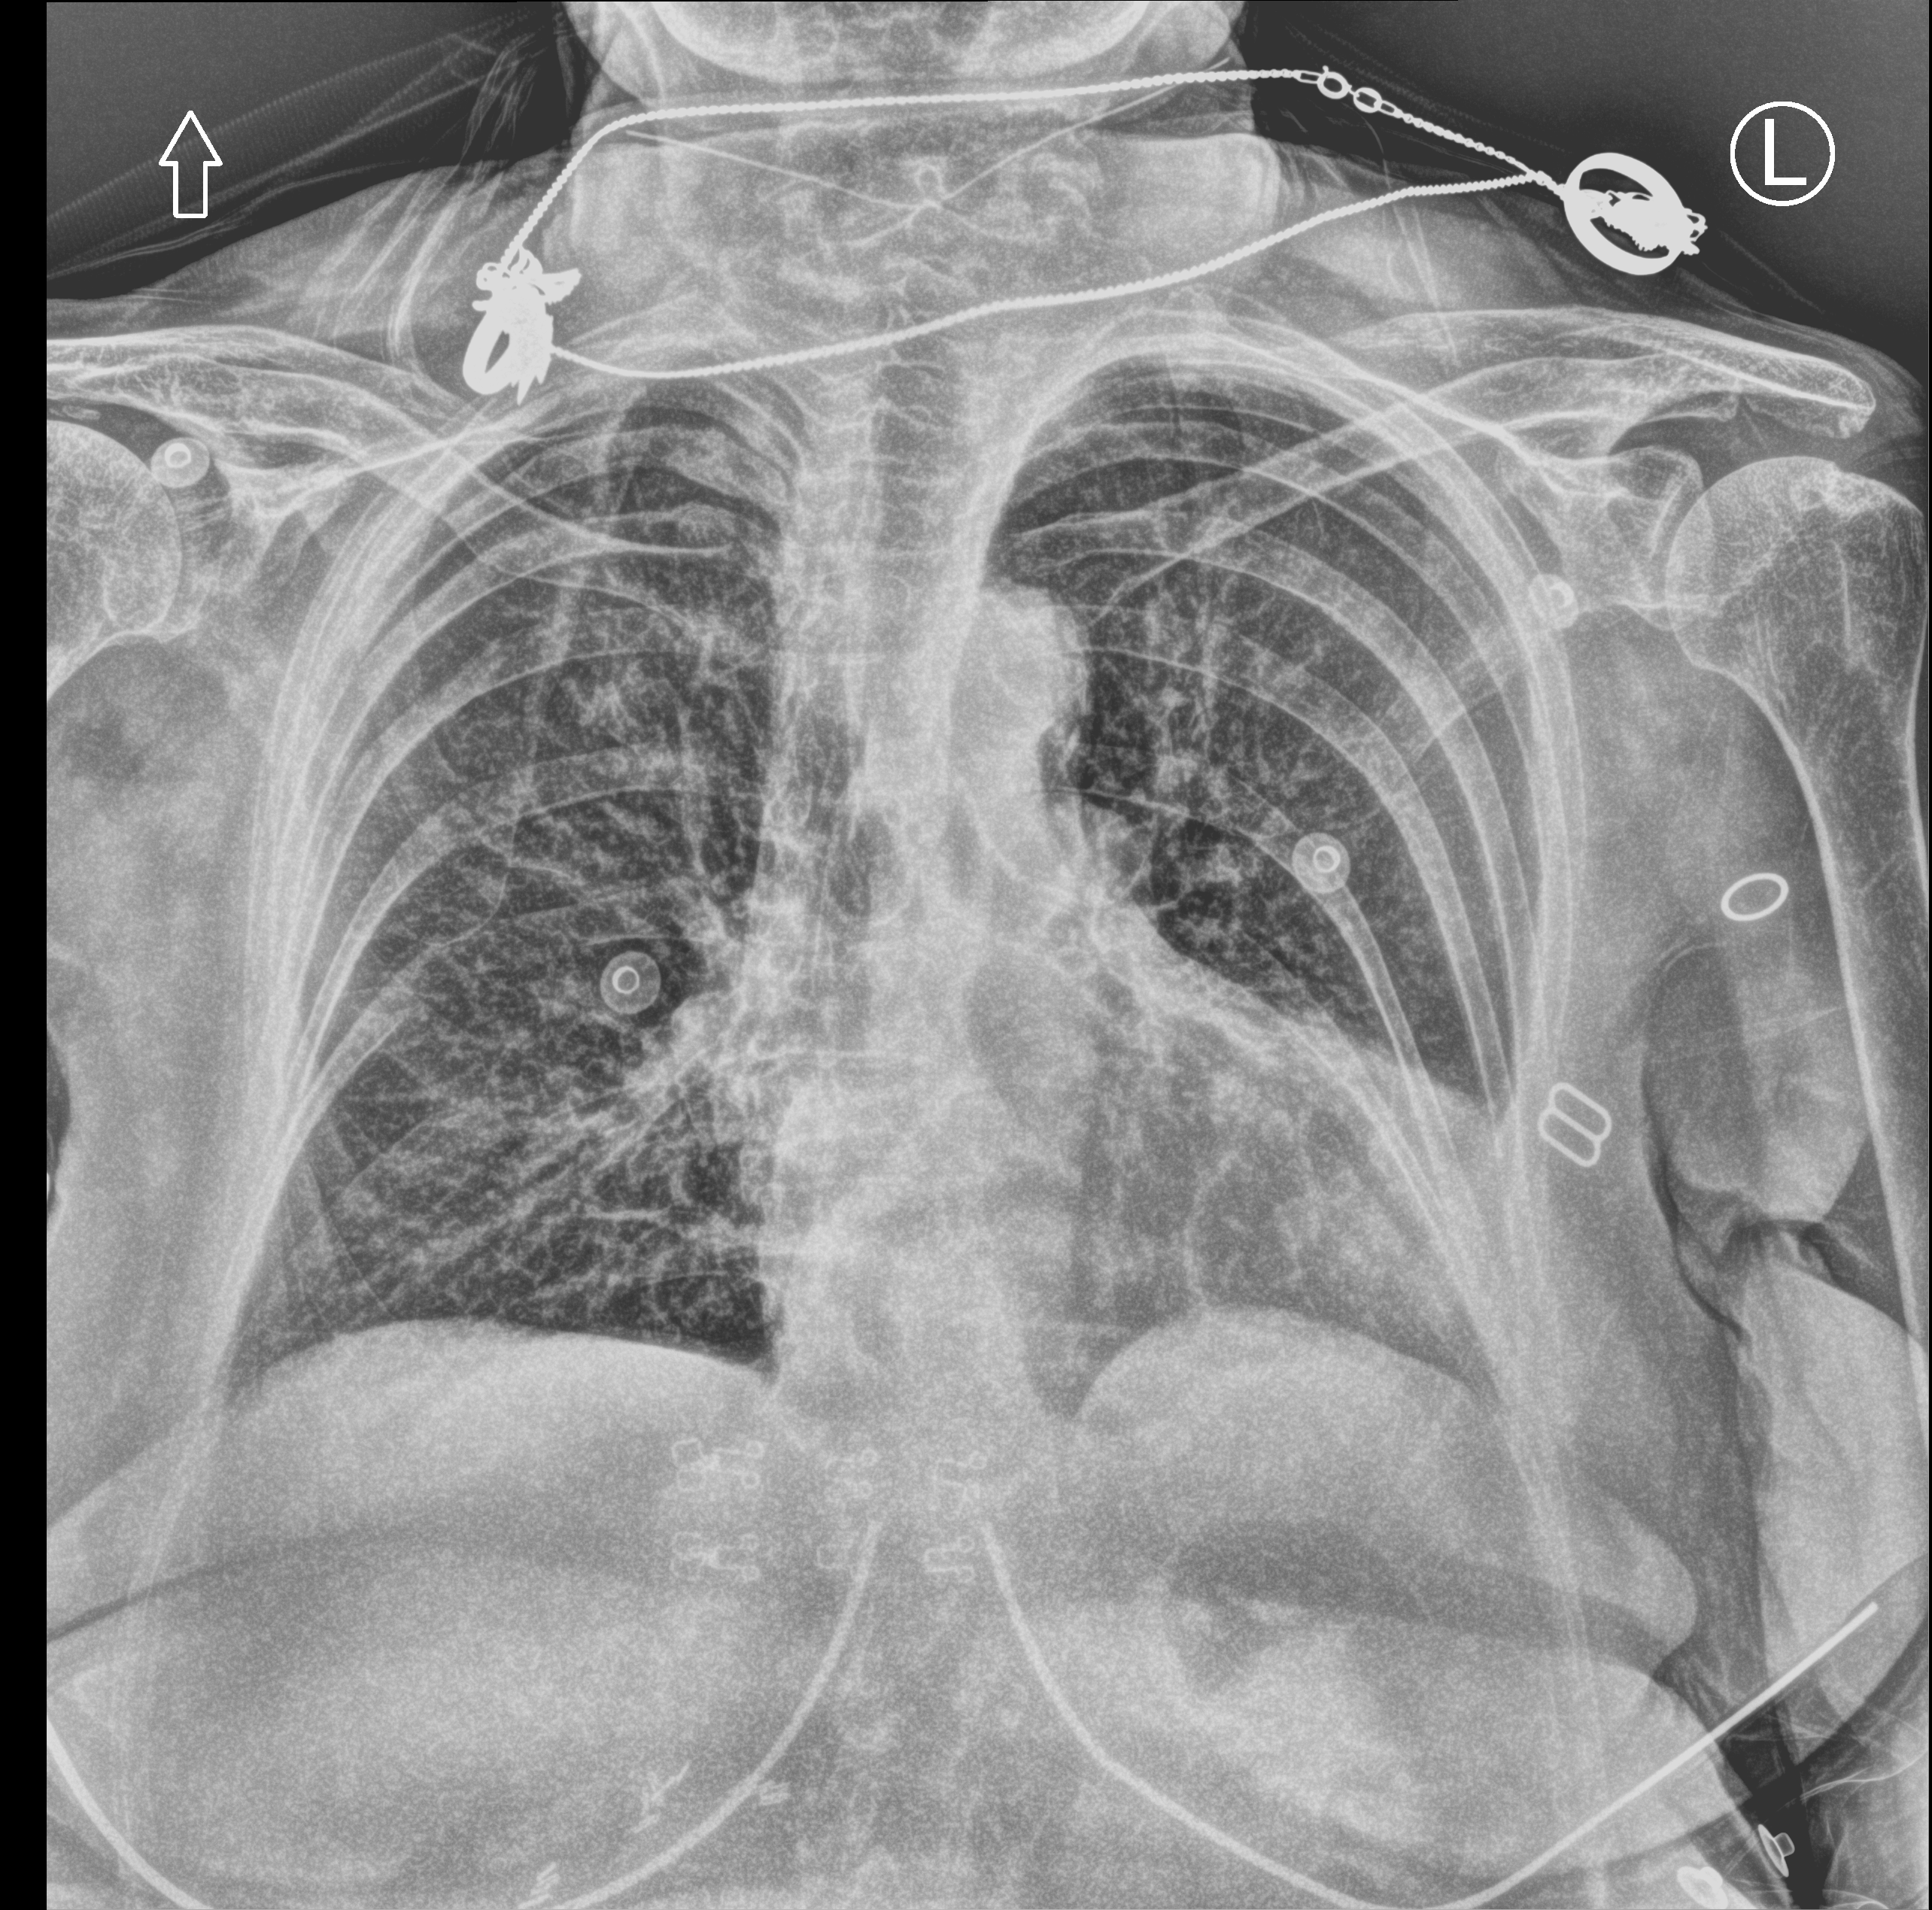
Chest X-ray (portable). Female patient hospitalised with COVID-19, age 75–90 years.
Admission-level facts for this patient (not findings on this image; timing relative to this image not recorded): hypertension (admission record): yes; chronic kidney disease (admission record): no.